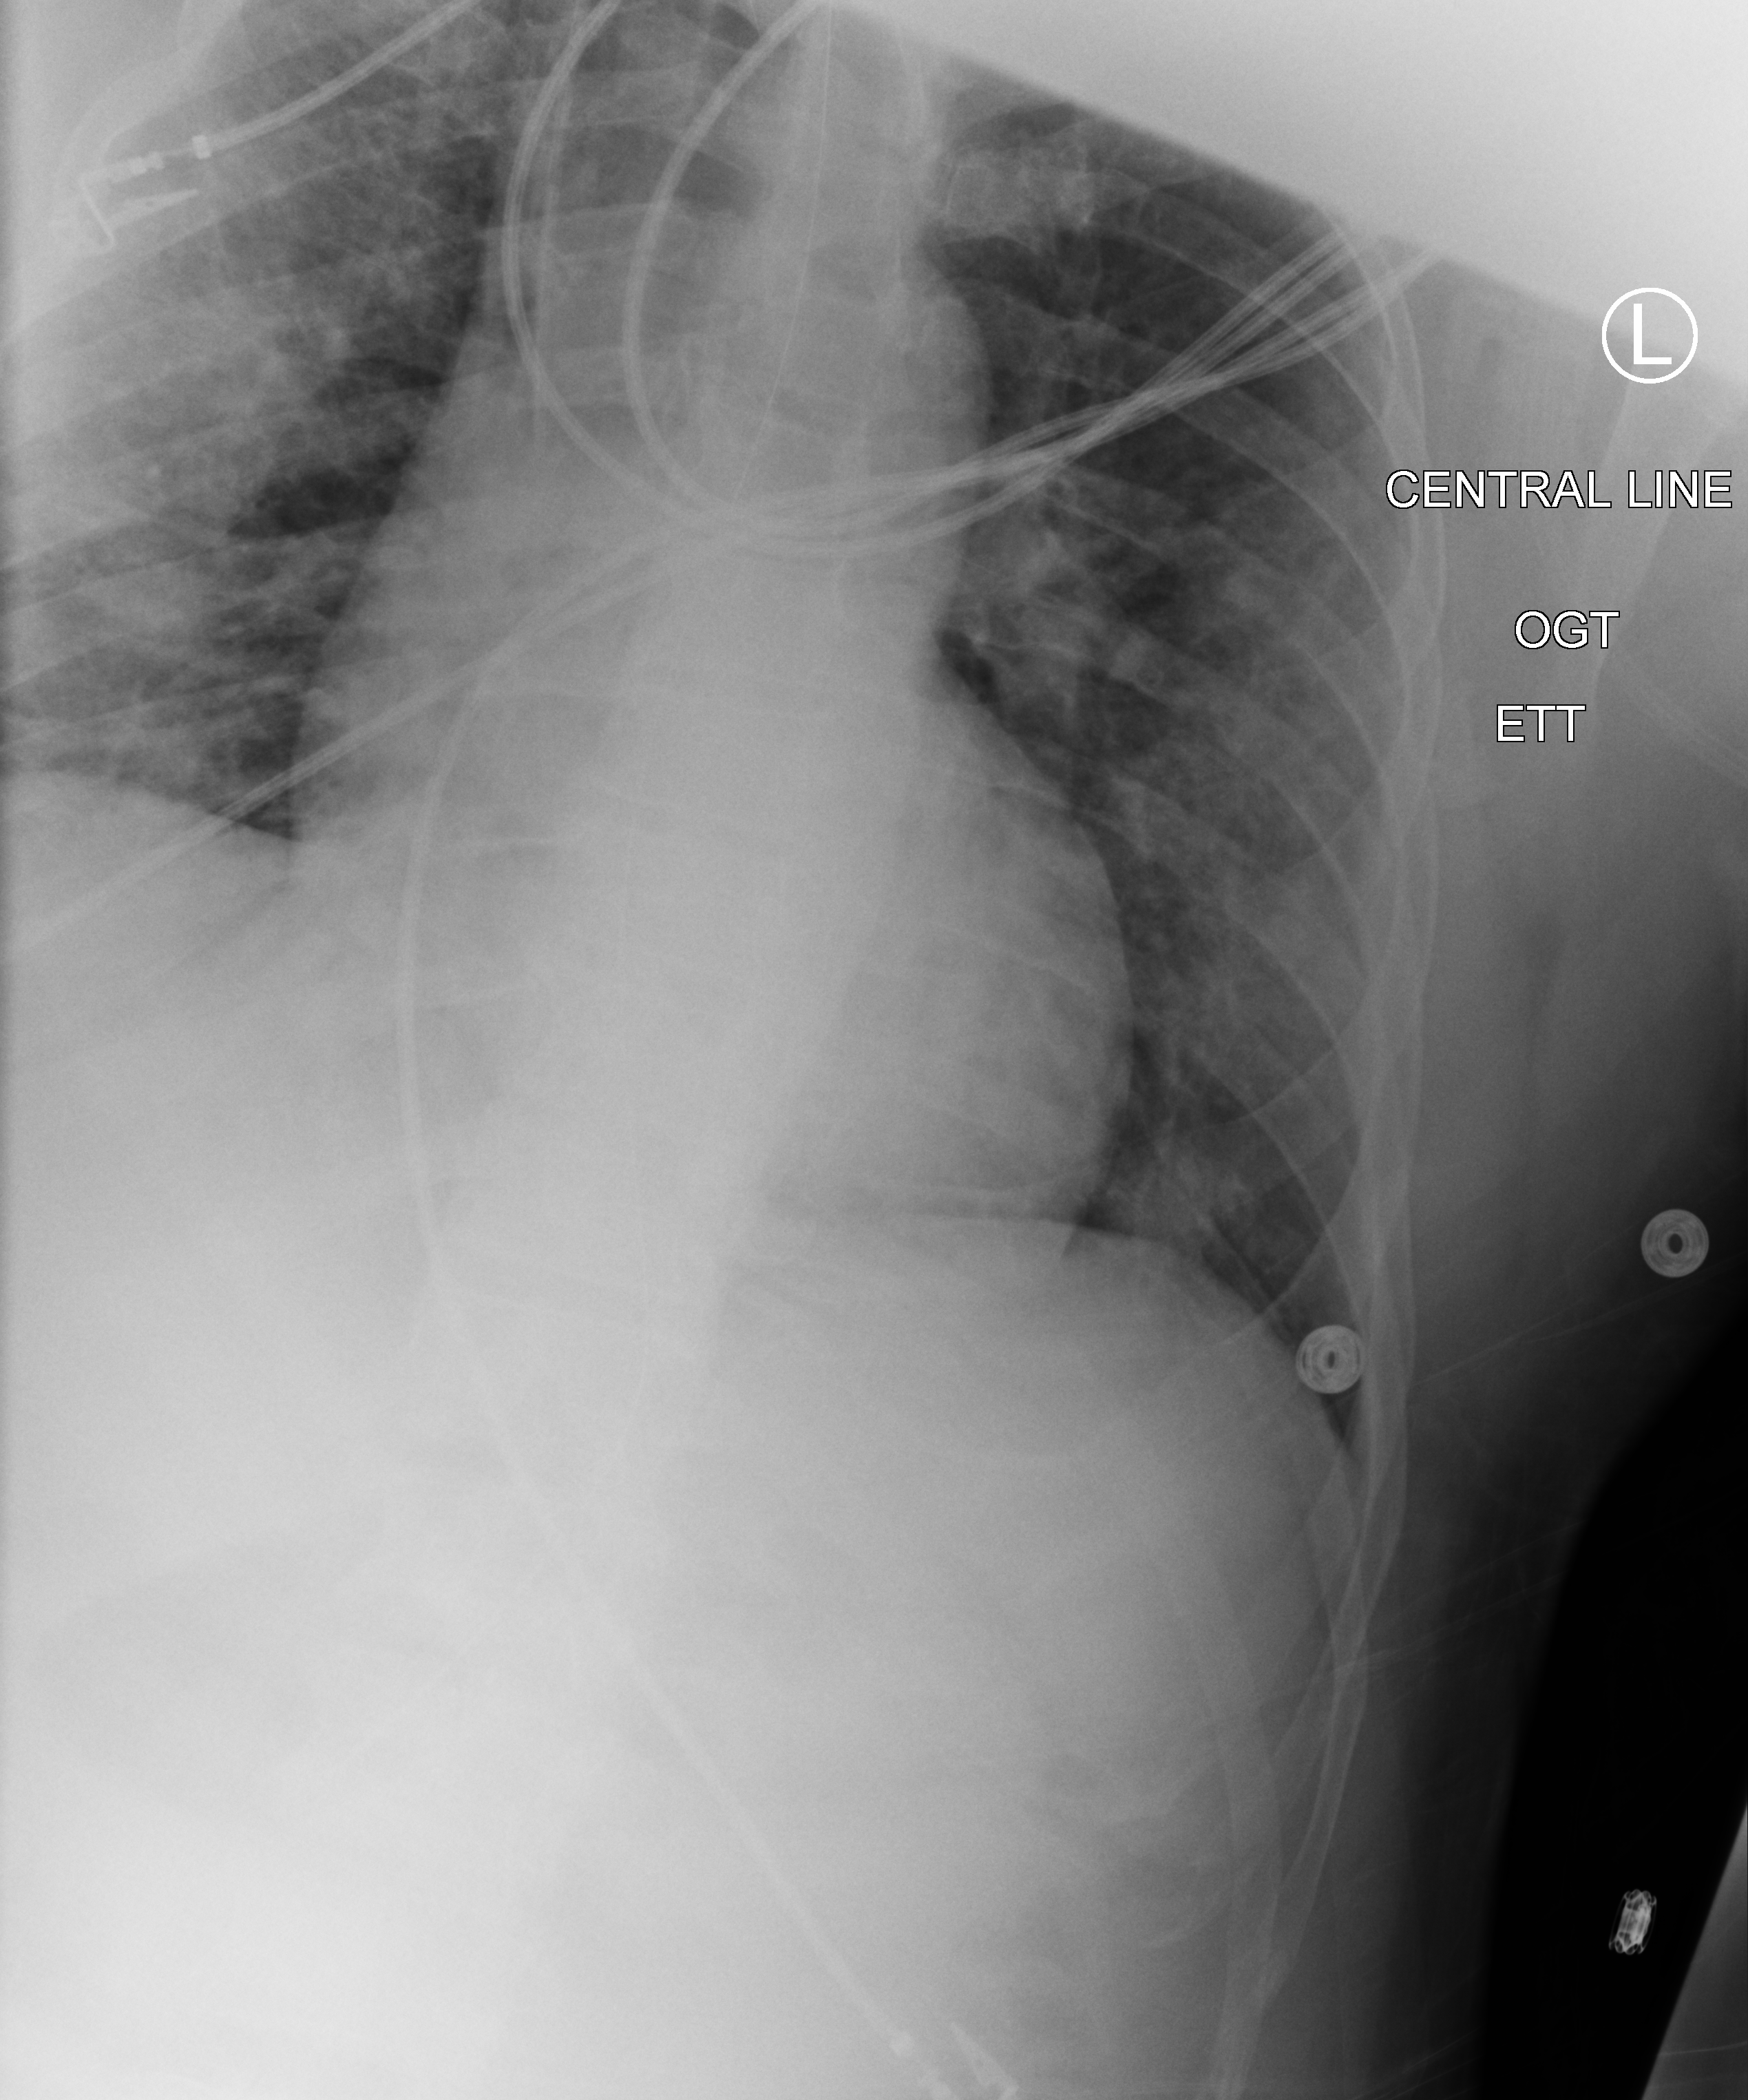
Portable chest radiograph, anteroposterior (AP) projection. Male patient hospitalised with COVID-19, age 18–59 years.
From the hospital-stay record, not from the radiograph (when in the stay this image was taken is not recorded):
- admitted to intensive care during this hospital stay: no